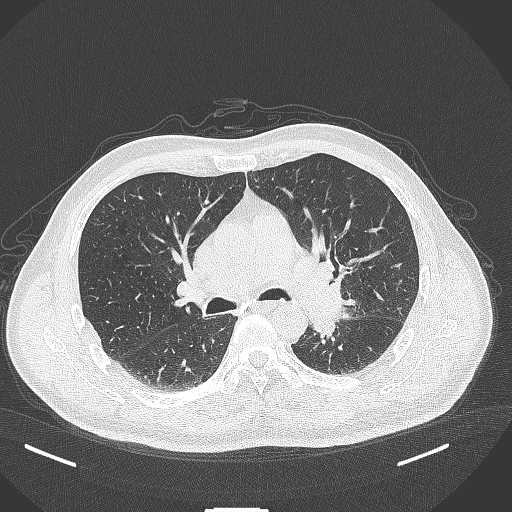
Chest CT, one axial slice; reconstruction kernel B70f; 120 kVp; lung window (W 1500 / L -600 HU); 1 mm slice thickness; 512 × 512 image matrix, field of view 400 × 400 mm. Patient: male, 55 years. From the clinical record (not read from this slice): clinical TNM (as recorded): T3 N0 M1c; histopathological grade: G3.
Annotated regions visible in this slice (rectangle marked by the reading radiologist):
- lung tumour (recorded histology: adenocarcinoma): bounding box (x1, y1, x2, y2) in pixels: (303, 300, 342, 339)